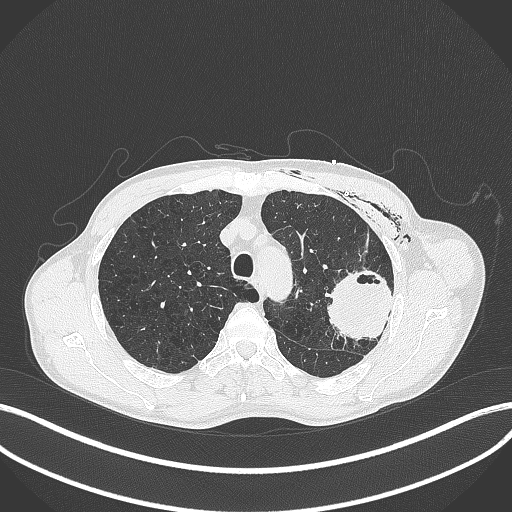
Chest CT, one axial slice; slice 310 of 457 in the series (ordered by position); lung window (W 1500 / L -600 HU); 1 mm slice thickness; 512 × 512 image matrix, field of view 400 × 400 mm. Male patient, age 58 years. From the clinical record (not read from this slice): clinical TNM (as recorded): T3 N0 M0.
Outlined on this slice (bounding box drawn by a radiologist):
- lung tumour (recorded histology: adenocarcinoma): bounding box <325,268,399,345> (left, top, right, bottom; pixels)